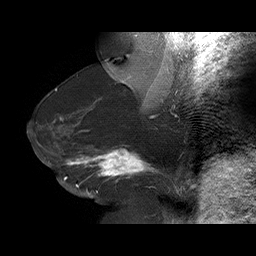
Breast MRI (dynamic contrast-enhanced), one sagittal slice; slice 39 of 75 in the series (ordered by position); dynamic contrast-enhanced series, time point 2 of 6 at this slice position (early post-contrast); 1.5 T; TE 4.5 ms, TR 32.4 ms; 3 mm slice thickness; 256 × 256 image matrix, field of view 180 × 180 mm. Female patient. From the clinical record (not read from this slice): setting: breast cancer imaged before/during neoadjuvant chemotherapy; receptor status: HR-positive, HER2-negative.
Annotated regions visible in this slice (semi-automatic segmentation, software-assisted and operator-edited):
- analysis volume of interest (the breast-tissue region the enhancement analysis was run in; not a lesion): bounding box <58,134,166,191> (left, top, right, bottom; pixels)
- tumour enhancement mask (voxels above the 100 % enhancement threshold inside the analysis volume of interest): <64,148,153,187>